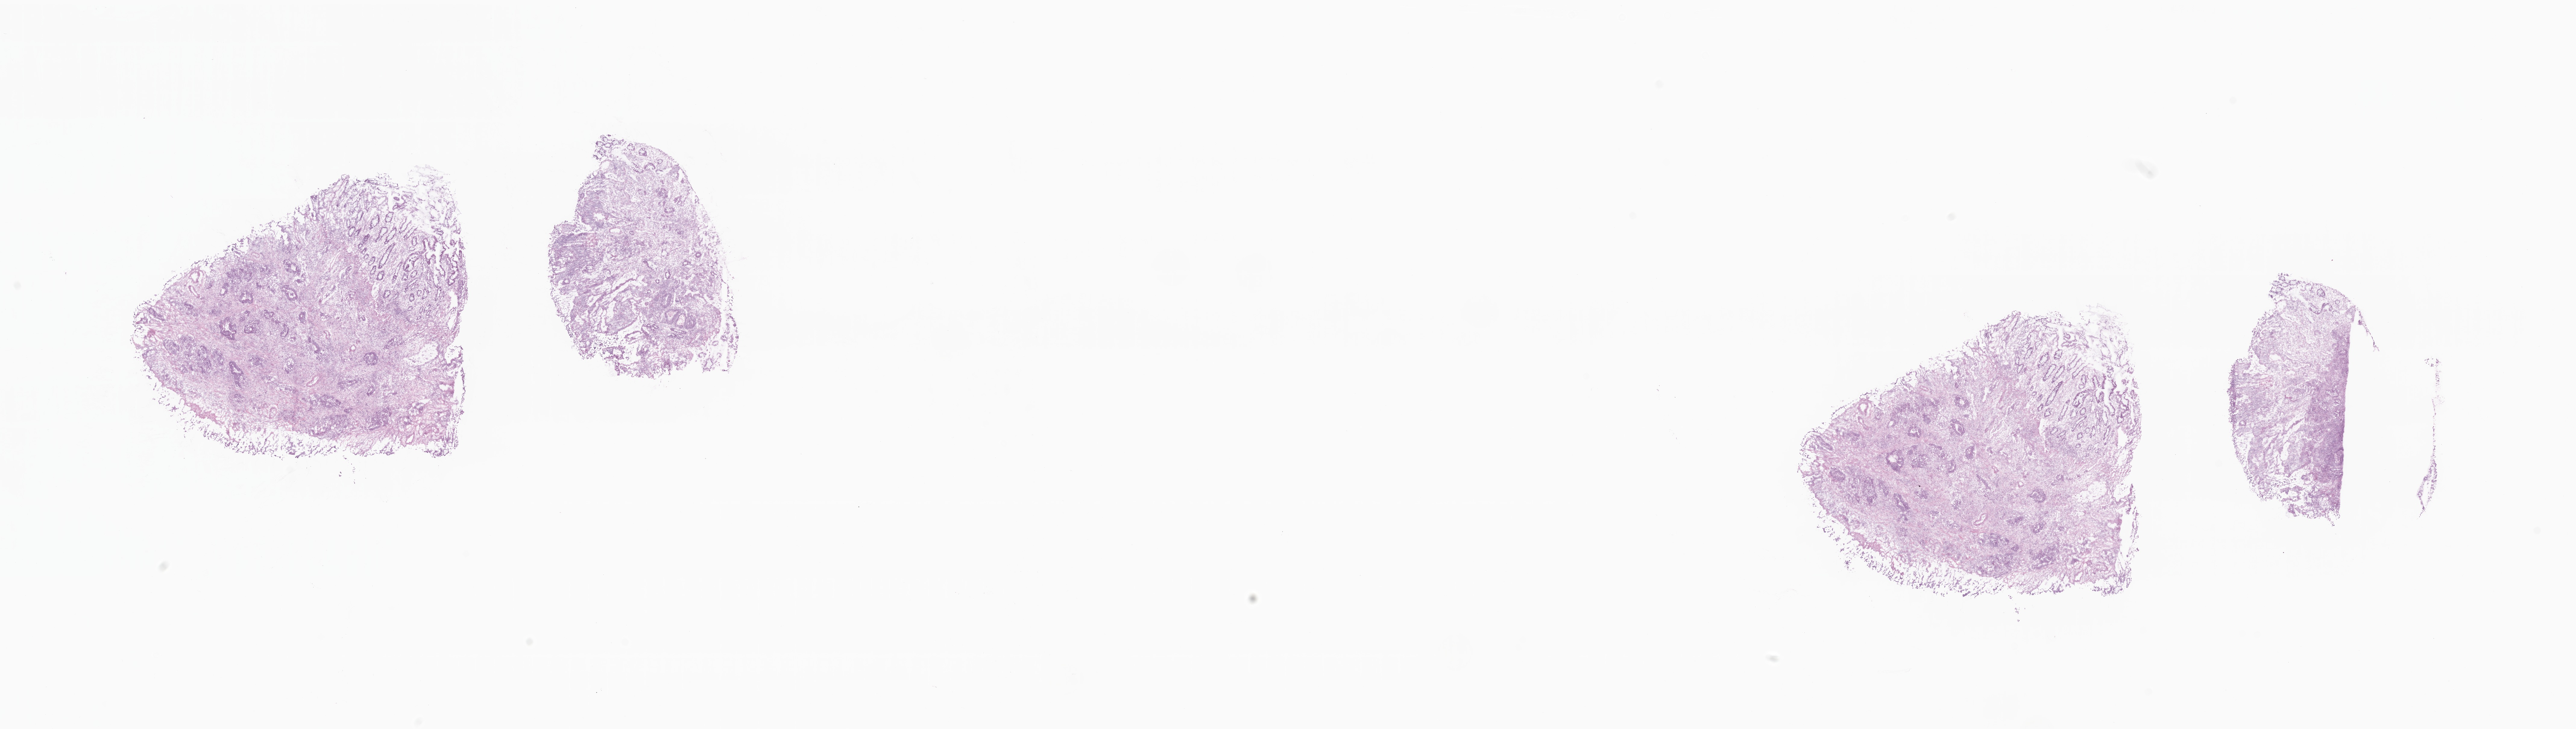
Digitized hematoxylin and eosin (H&E)-stained section — low-resolution overview of the scanned area, about 36.0 x 10.2 mm, cryosection, specimen: primary tumor, anatomic site: sigmoid colon. Patient: female, age at initial diagnosis 76 years. Composition of this section per pathologist review: tumor cells 28%, tumor nuclei 45%, stromal cells 57%, necrosis 5%, normal cells 10%. Infiltration values recorded for this section: lymphocyte infiltration 45%, monocyte infiltration 2%, neutrophil infiltration 0%.
* section: bottom of the tissue portion
* diagnosis: Adenocarcinoma, NOS